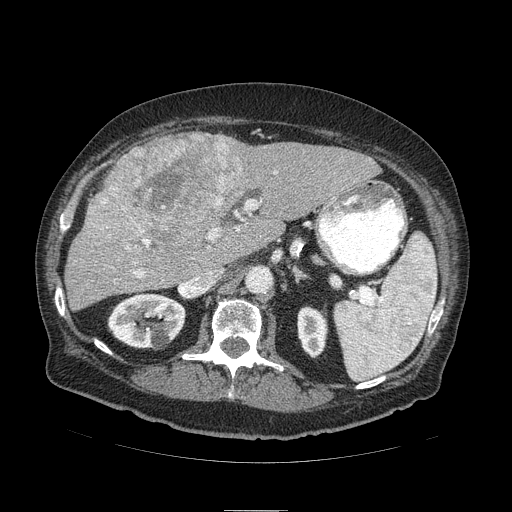
Contrast-enhanced abdominal CT (liver protocol), one axial slice; position 53 of 103 along the scan axis; 120 kVp; soft-tissue window (W 400 / L 40 HU); 2.5 mm slice thickness; 512 × 512 image matrix. Case-level facts recorded for this patient, not image findings: diagnosis: hepatocellular carcinoma (patient treated with transarterial chemoembolisation; whether this scan precedes or follows treatment is not stated here); TNM stage (as recorded): Stage-IIIA; Child-Pugh class: B; tumour nodularity: multinodular.
Annotated regions visible in this slice (semi-automatically segmented with operator editing):
- liver parenchyma outside the tumour (the mass and vessels are separate outlines, so this box may not span the whole liver): bounding box [x1, y1, x2, y2] px = [64, 134, 378, 310]
- mass: [84, 131, 247, 251]
- liver vessels: [127, 172, 276, 278]